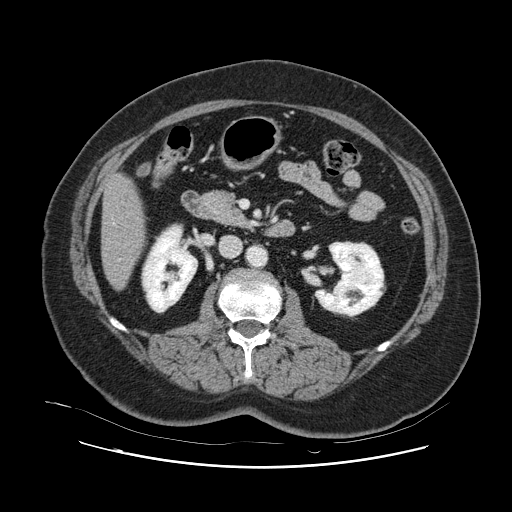
Contrast-enhanced abdominal CT, one axial slice. Slice 31 of 132 in the series (ordered by position). Intravenous contrast given. Soft-tissue window (W 400 / L 40 HU). 2.5 mm slice thickness. 512 × 512 image matrix, field of view 391 × 391 mm. Female patient, age 73 years. Case-level facts recorded for this patient, not image findings: diagnosis: colorectal cancer liver metastases, imaged before liver resection; multiple liver metastases: no; largest metastasis: 7 cm.
Outlined on this slice (outlined manually by an expert reader):
- hepatic veins: bounding box (x1, y1, x2, y2) in pixels: (113, 223, 115, 226)
- liver: (102, 177, 145, 289)
- planned liver remnant (the part of the liver to remain after resection): (102, 176, 146, 289)